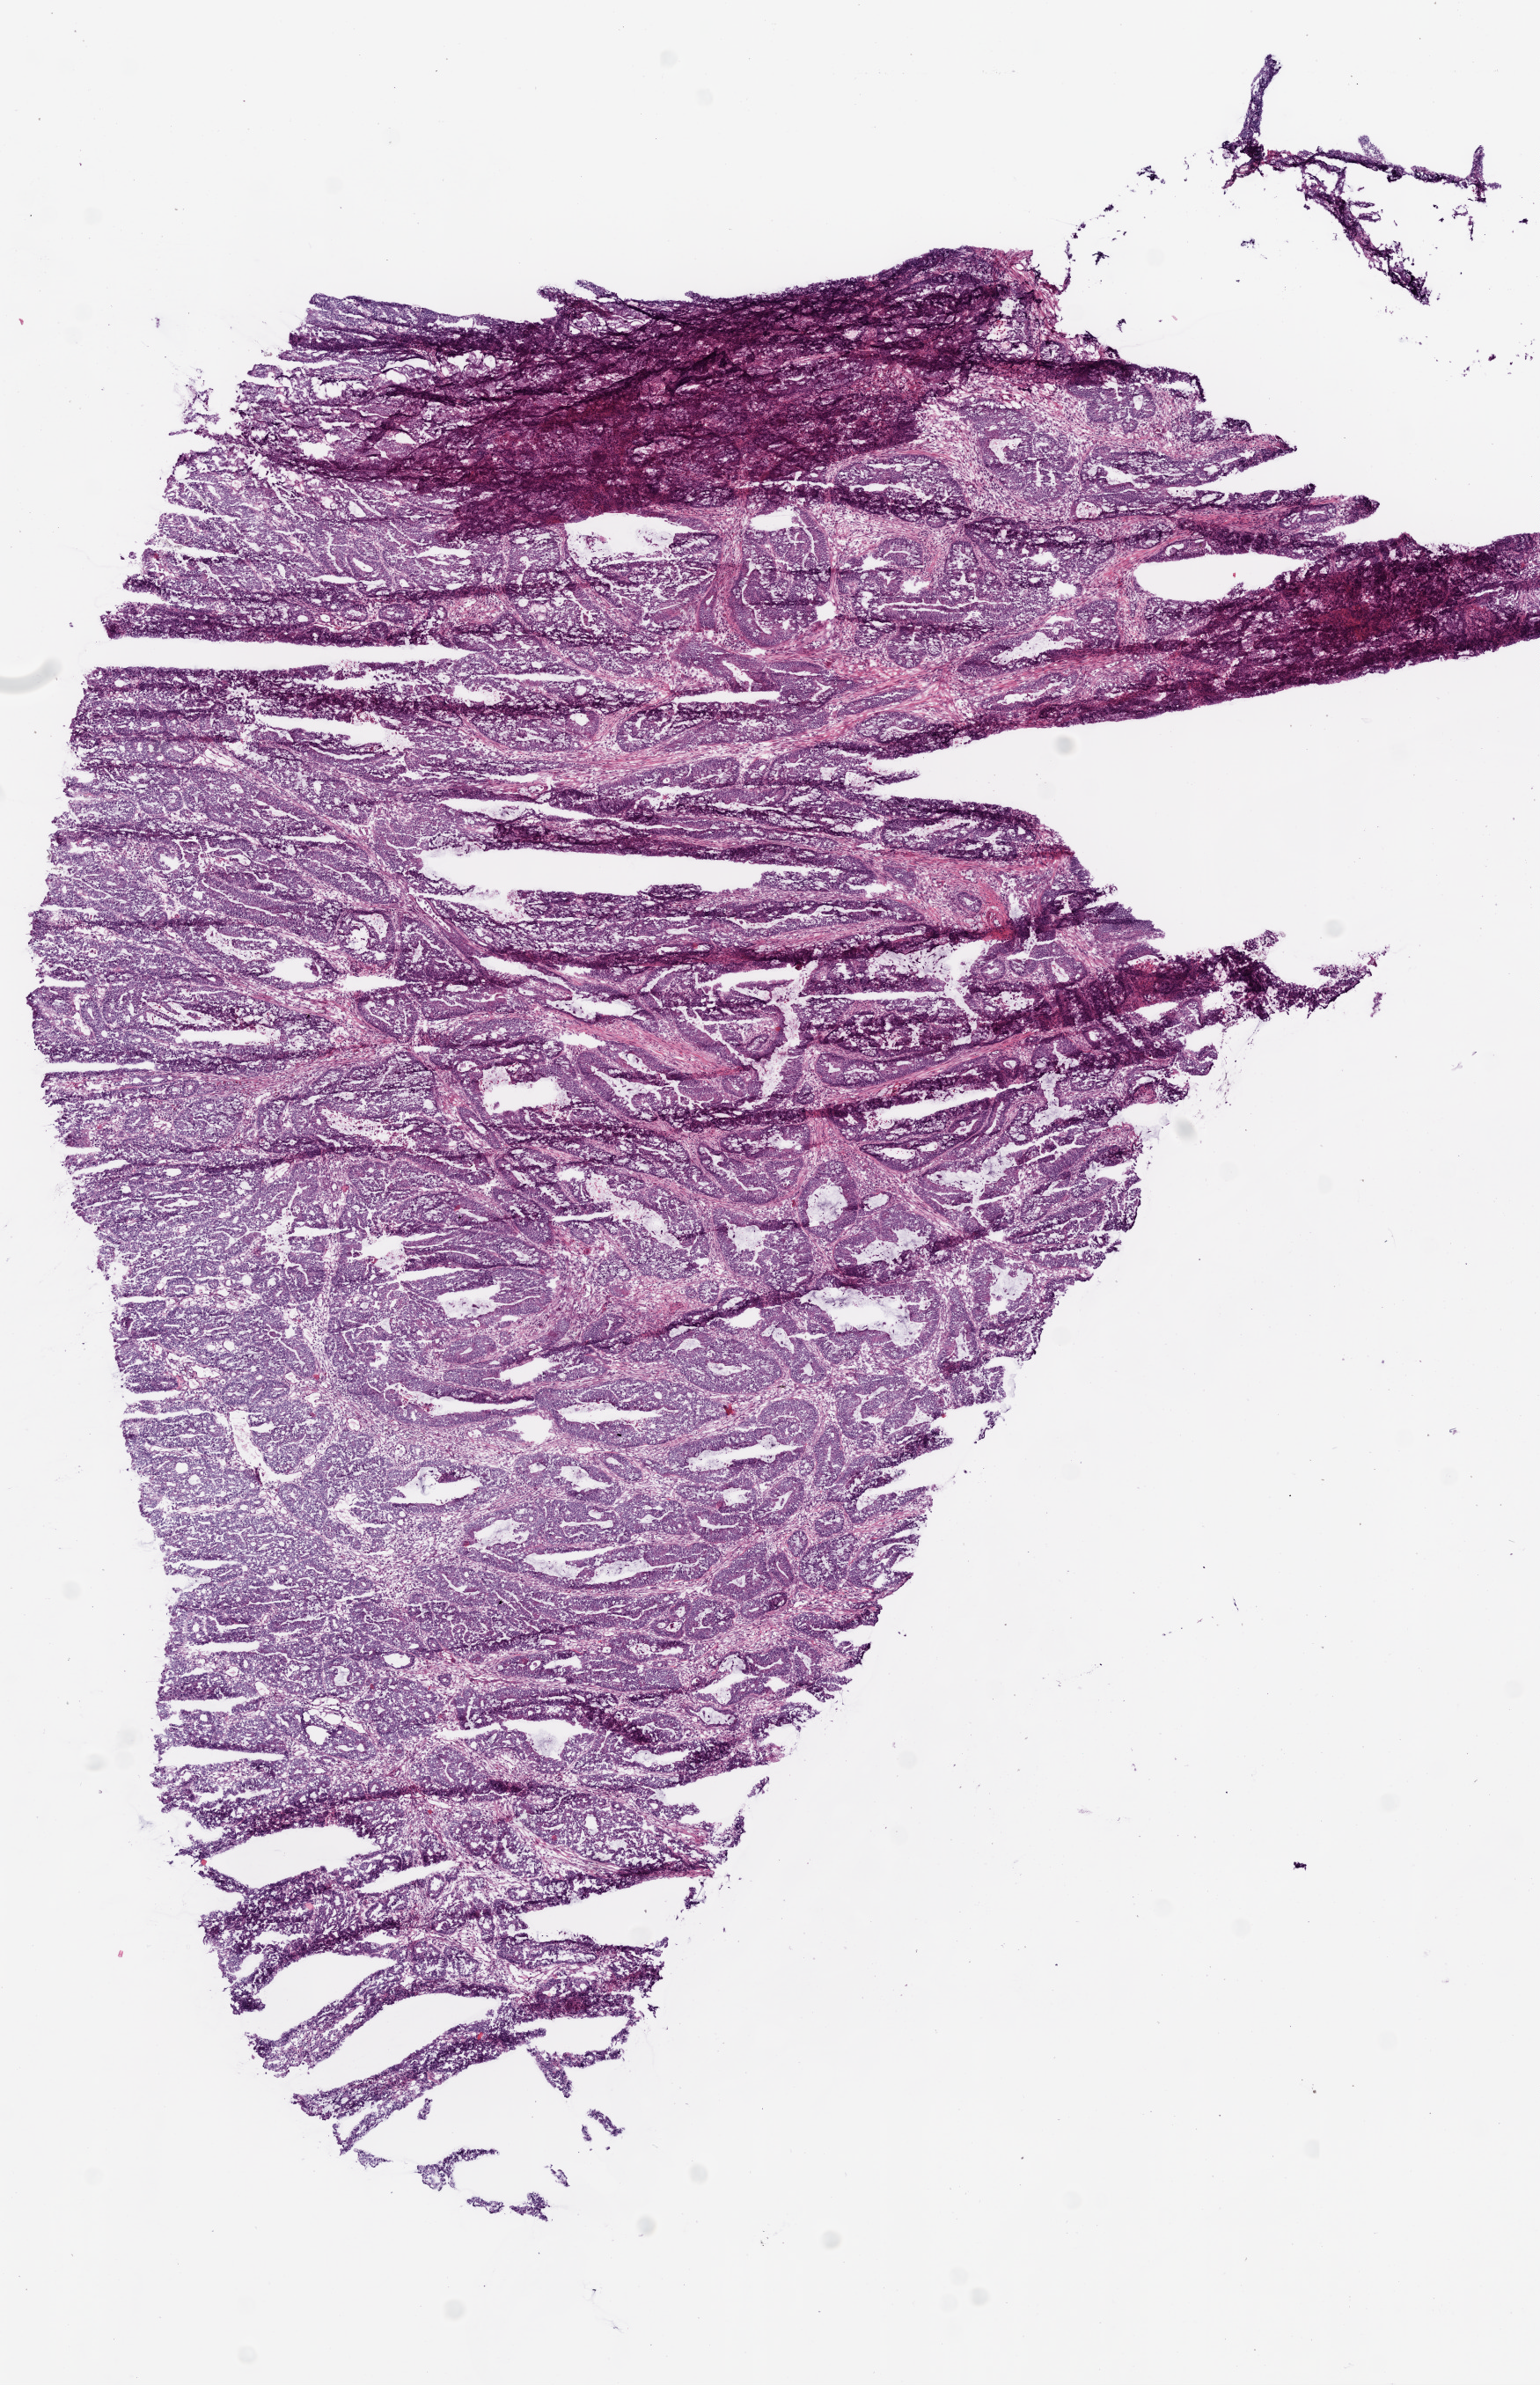
Whole-slide histology image, H&E-stained, shown as a low-resolution overview of the whole scanned area (about 7.0 x 10.9 mm). Frozen section. Primary tumour sample from the colon. Male, age 68 years at initial diagnosis. Pathologist review of this section (percent, as recorded): tumour cells 90%, tumour nuclei 95%, normal cells 0%, stromal cells 10%, necrosis 0%.
Pathologic diagnosis: Adenocarcinoma, NOS (sigmoid colon). AJCC pathologic stage: II (5th edition).